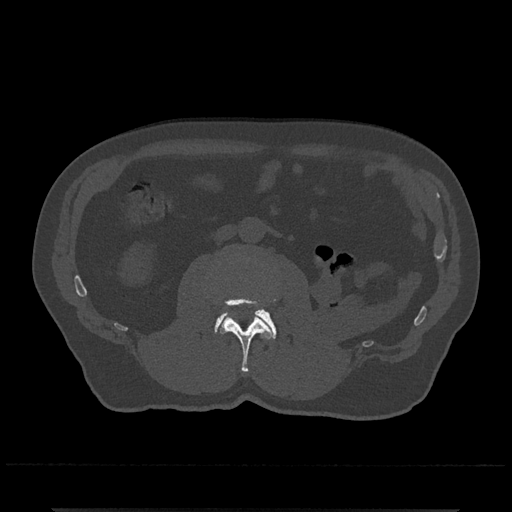
CT including the spine, one axial slice; position 267 of 797 along the scan axis; reconstruction kernel Br40s/3; bone window (W 1800 / L 400 HU); 512 × 512 image matrix. Male patient, age 67 years. Case-level facts recorded for this patient, not image findings: primary cancer: prostate.
Outlined on this slice (semi-automatically segmented with operator editing):
- L2 vertebra: bounding box [x1, y1, x2, y2] px = [221, 297, 276, 373]
- L3 vertebra: [214, 309, 277, 339]